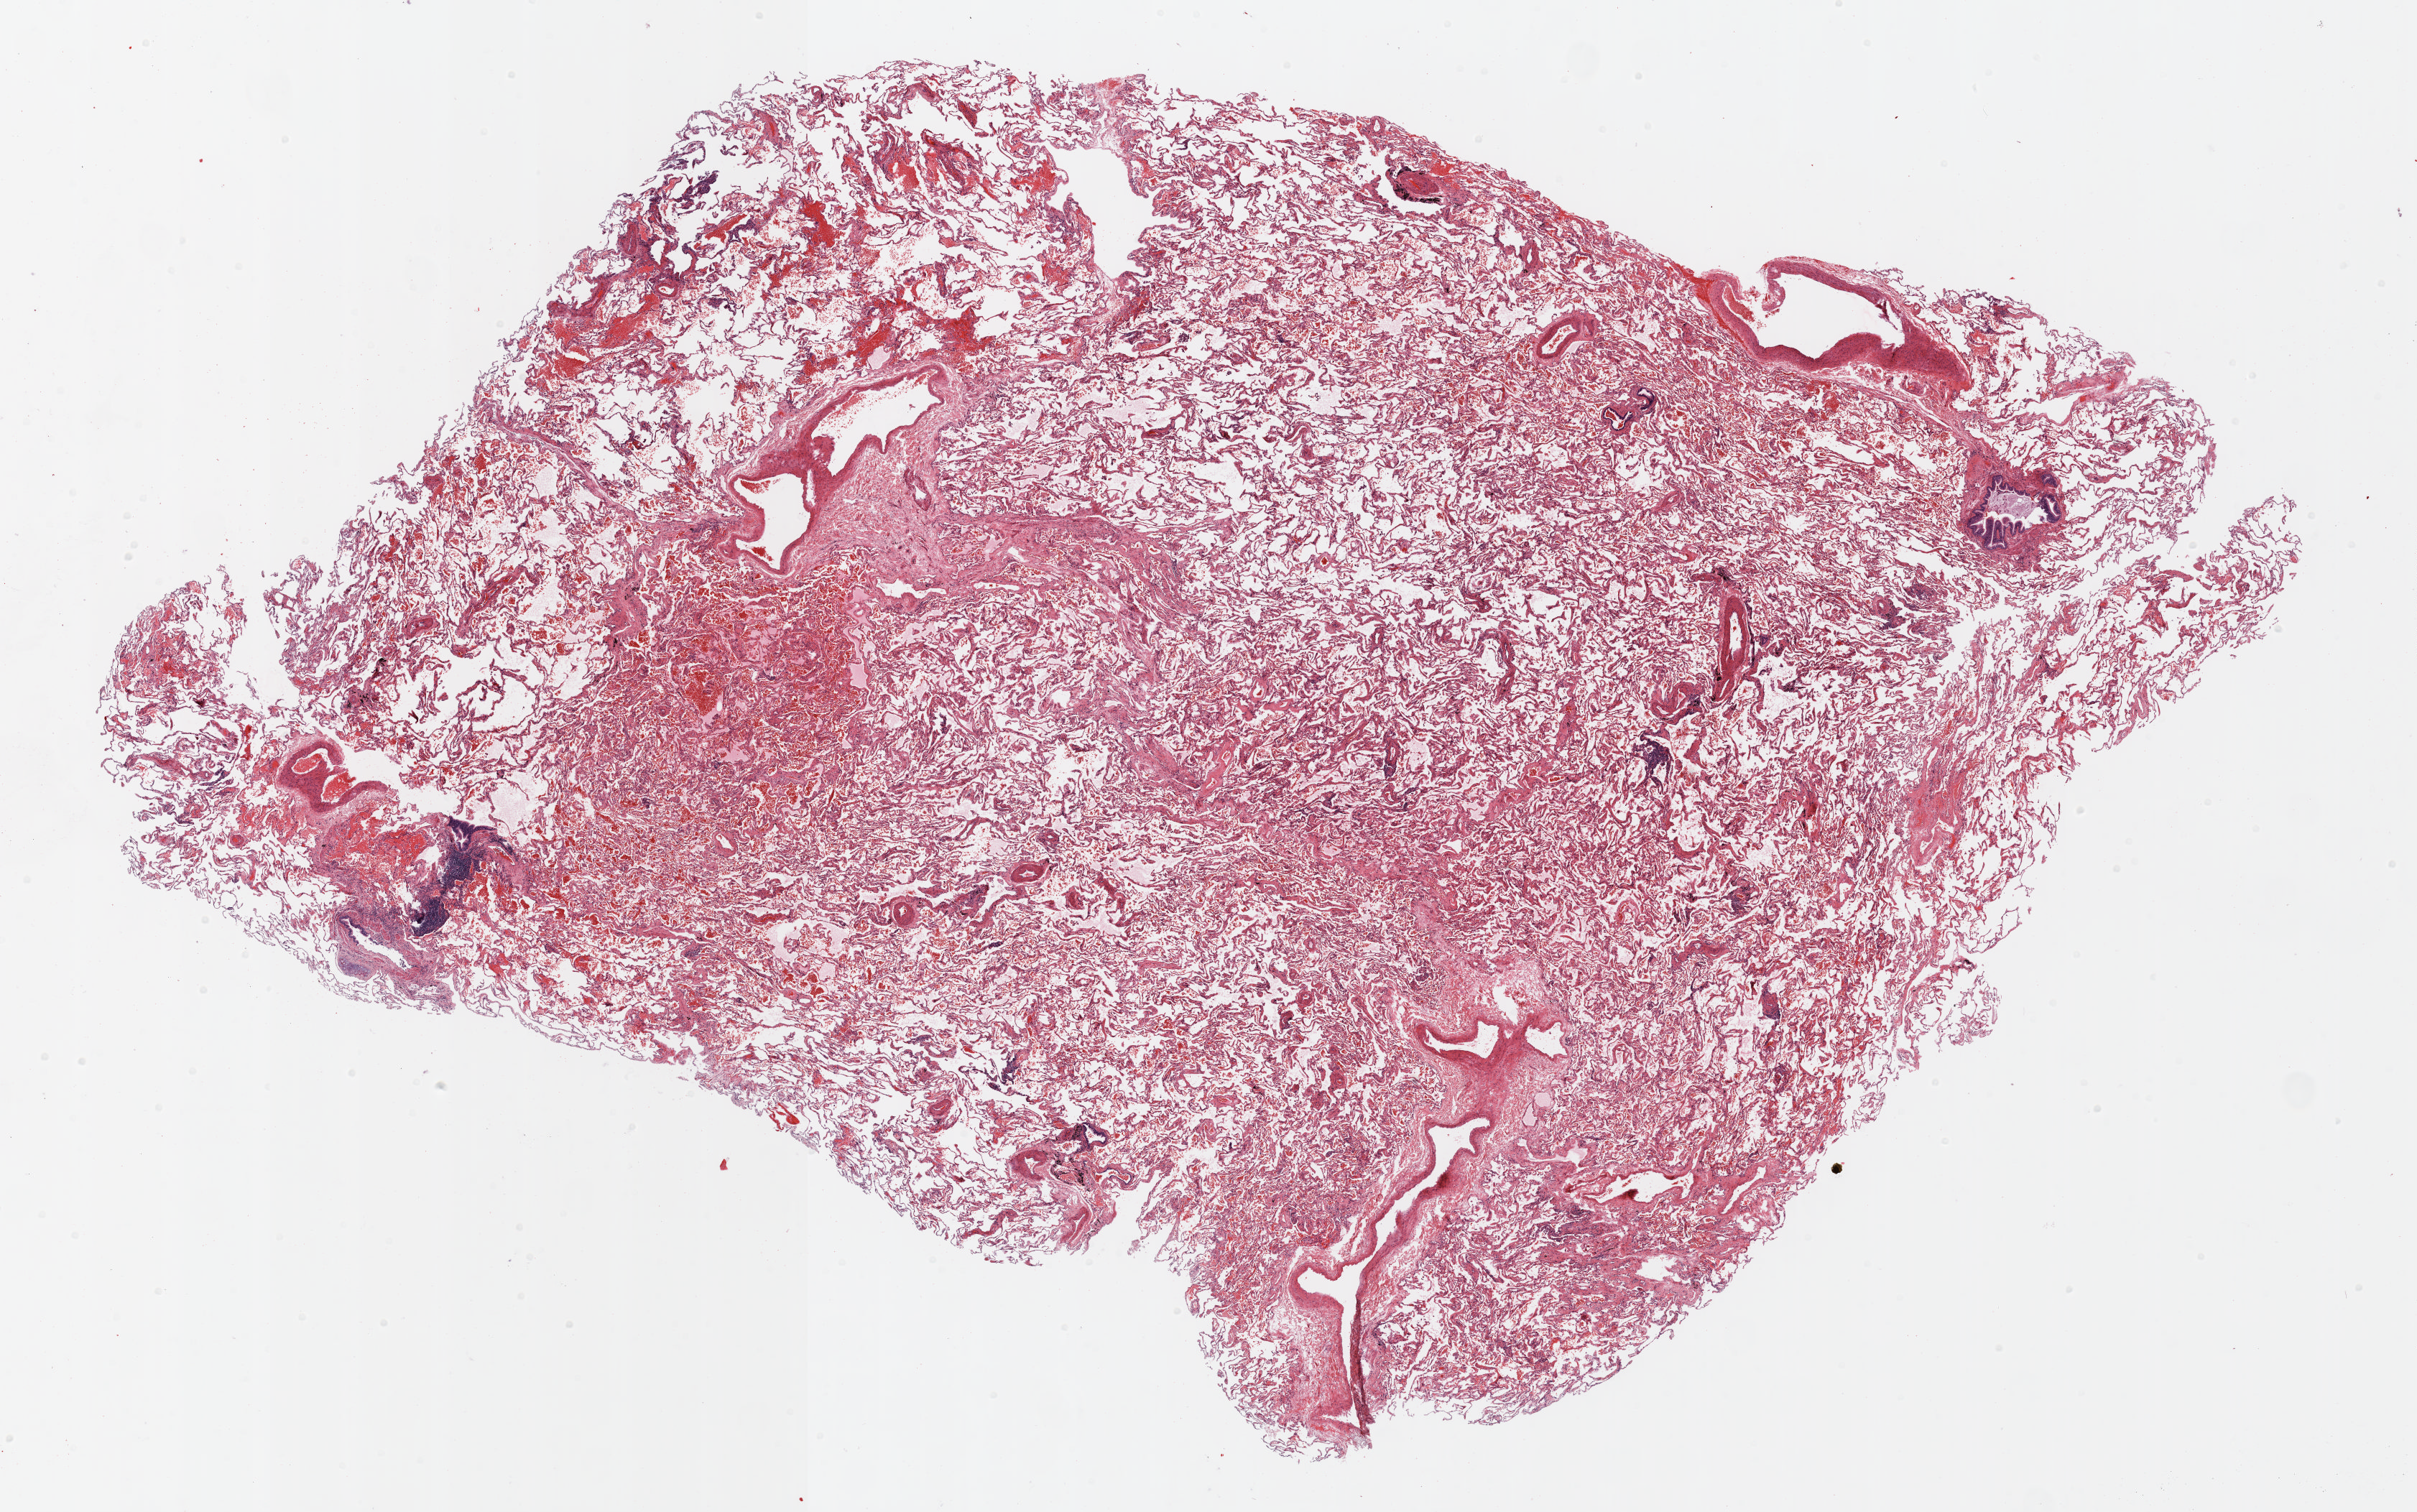
Whole-slide histology image, Hematoxylin and eosin (H&E) stained, a low-resolution overview of the entire scanned area, about 27.0 x 16.9 mm (slide scanned at 20x). Formalin-fixed paraffin-embedded (FFPE) section. Lung. Female patient, aged 67 at enrolment. Former smoker at enrolment. Grade: poorly differentiated (G3).
• participant's lung-cancer diagnosis: Squamous cell carcinoma, NOS (ICD-O-3 8070/3)
• ICD-O-3 topography: upper lobe of lung (C34.1)
• stage (AJCC 6th edition): IA
• tumour size (pathology): 25 mm
• primary tumour location (clinical record): left upper lobe